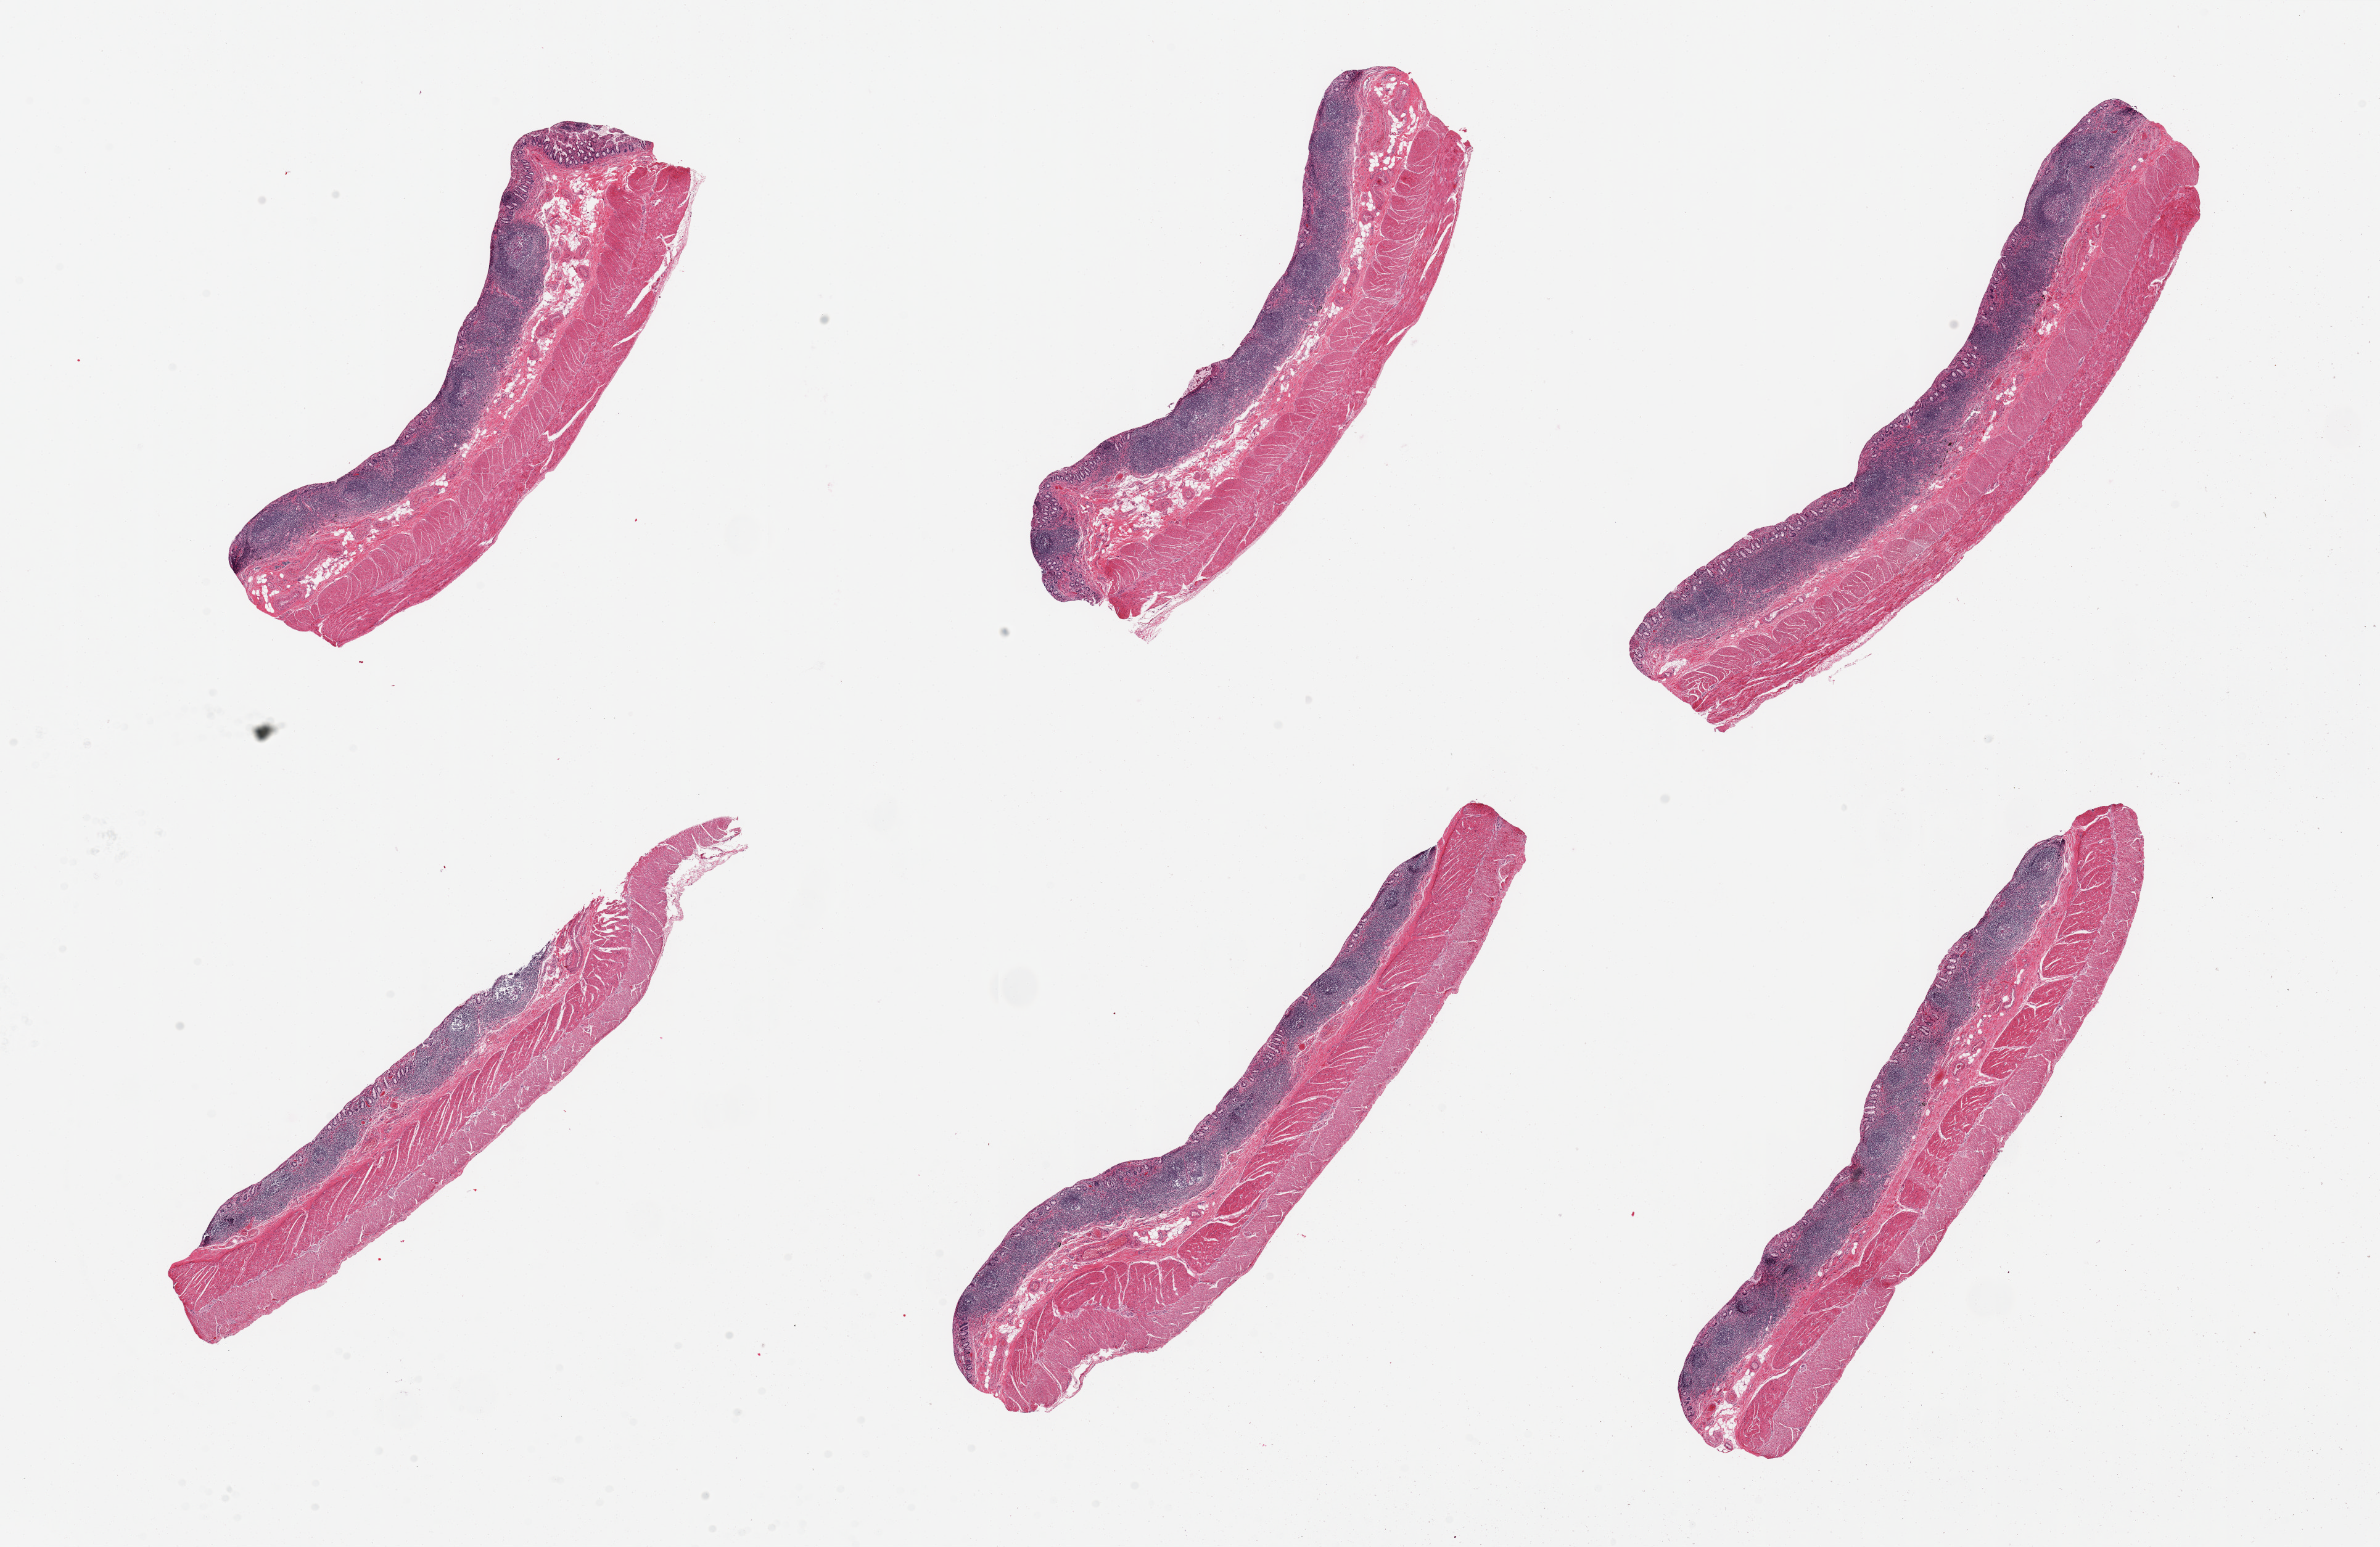
Digitized H&E-stained section — a low-resolution overview of the entire scanned area, about 30.5 x 19.8 mm (from a 20x scan), PAXgene-fixed, paraffin-embedded tissue, sampled site (target tissue): ileum, tissue donor sample. Female donor.
Reviewer comment on this tissue sample: 6 pieces, diffuse confluent lymphoid aggregates in all sections ~0.5mm thick, ~25% total volume; Surface mucosa nearl - total autolysis.